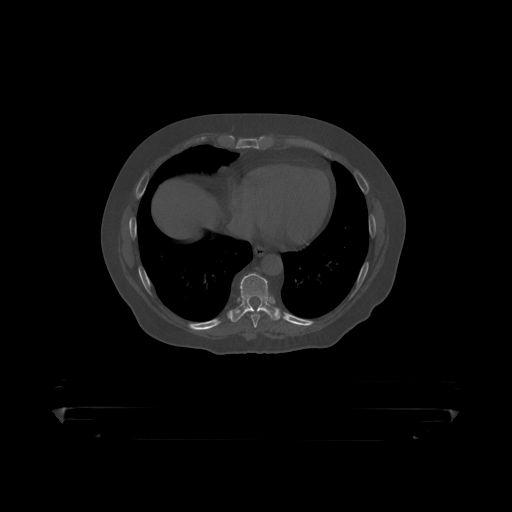
CT including the spine, one axial slice. Position 243 of 390 along the scan axis. Reconstruction kernel STANDARD. 120 kVp. Bone window (W 1800 / L 400 HU). 1.25 mm slice thickness. 512 × 512 image matrix. Patient: male, 60 years. Case-level facts recorded for this patient, not image findings: primary cancer: prostate.
Structures marked on this image (semi-automatically segmented with operator editing):
- T8 vertebra: bounding box (x1, y1, x2, y2) in pixels: (251, 315, 261, 319)
- T9 vertebra: (231, 273, 281, 317)